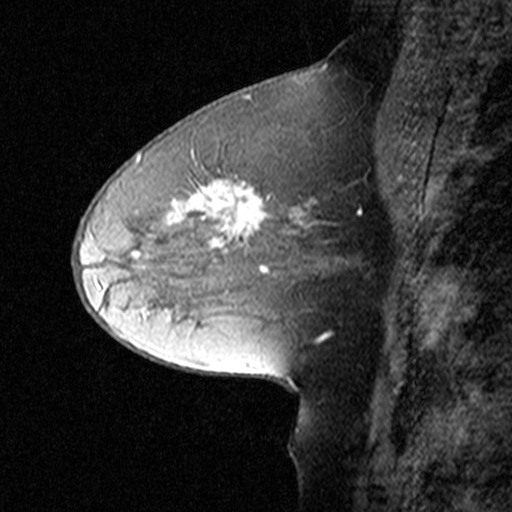
Breast MRI (dynamic contrast-enhanced), one sagittal slice. Slice 22 of 44 in the series (ordered by position). Dynamic contrast-enhanced study with each time point stored as its own series, time point 2 of 3 at this slice position (early post-contrast, ordered by acquisition time). 1.5 T. TE 4.5 ms, TR 11 ms. 3 mm slice thickness. 512 × 512 image matrix. Female patient, age 50 years. Case-level facts recorded for this patient, not image findings: setting: breast cancer imaged before/during neoadjuvant chemotherapy; receptor status: HR-positive, HER2-negative.
Annotated regions visible in this slice (semi-automatic segmentation, software-assisted and operator-edited):
- analysis volume of interest (the breast-tissue region the enhancement analysis was run in; not a lesion): box from (x=126, y=162) to (x=329, y=291) px
- tumour enhancement mask (voxels above the 90 % enhancement threshold inside the analysis volume of interest): (x=169, y=180)–(x=317, y=246)